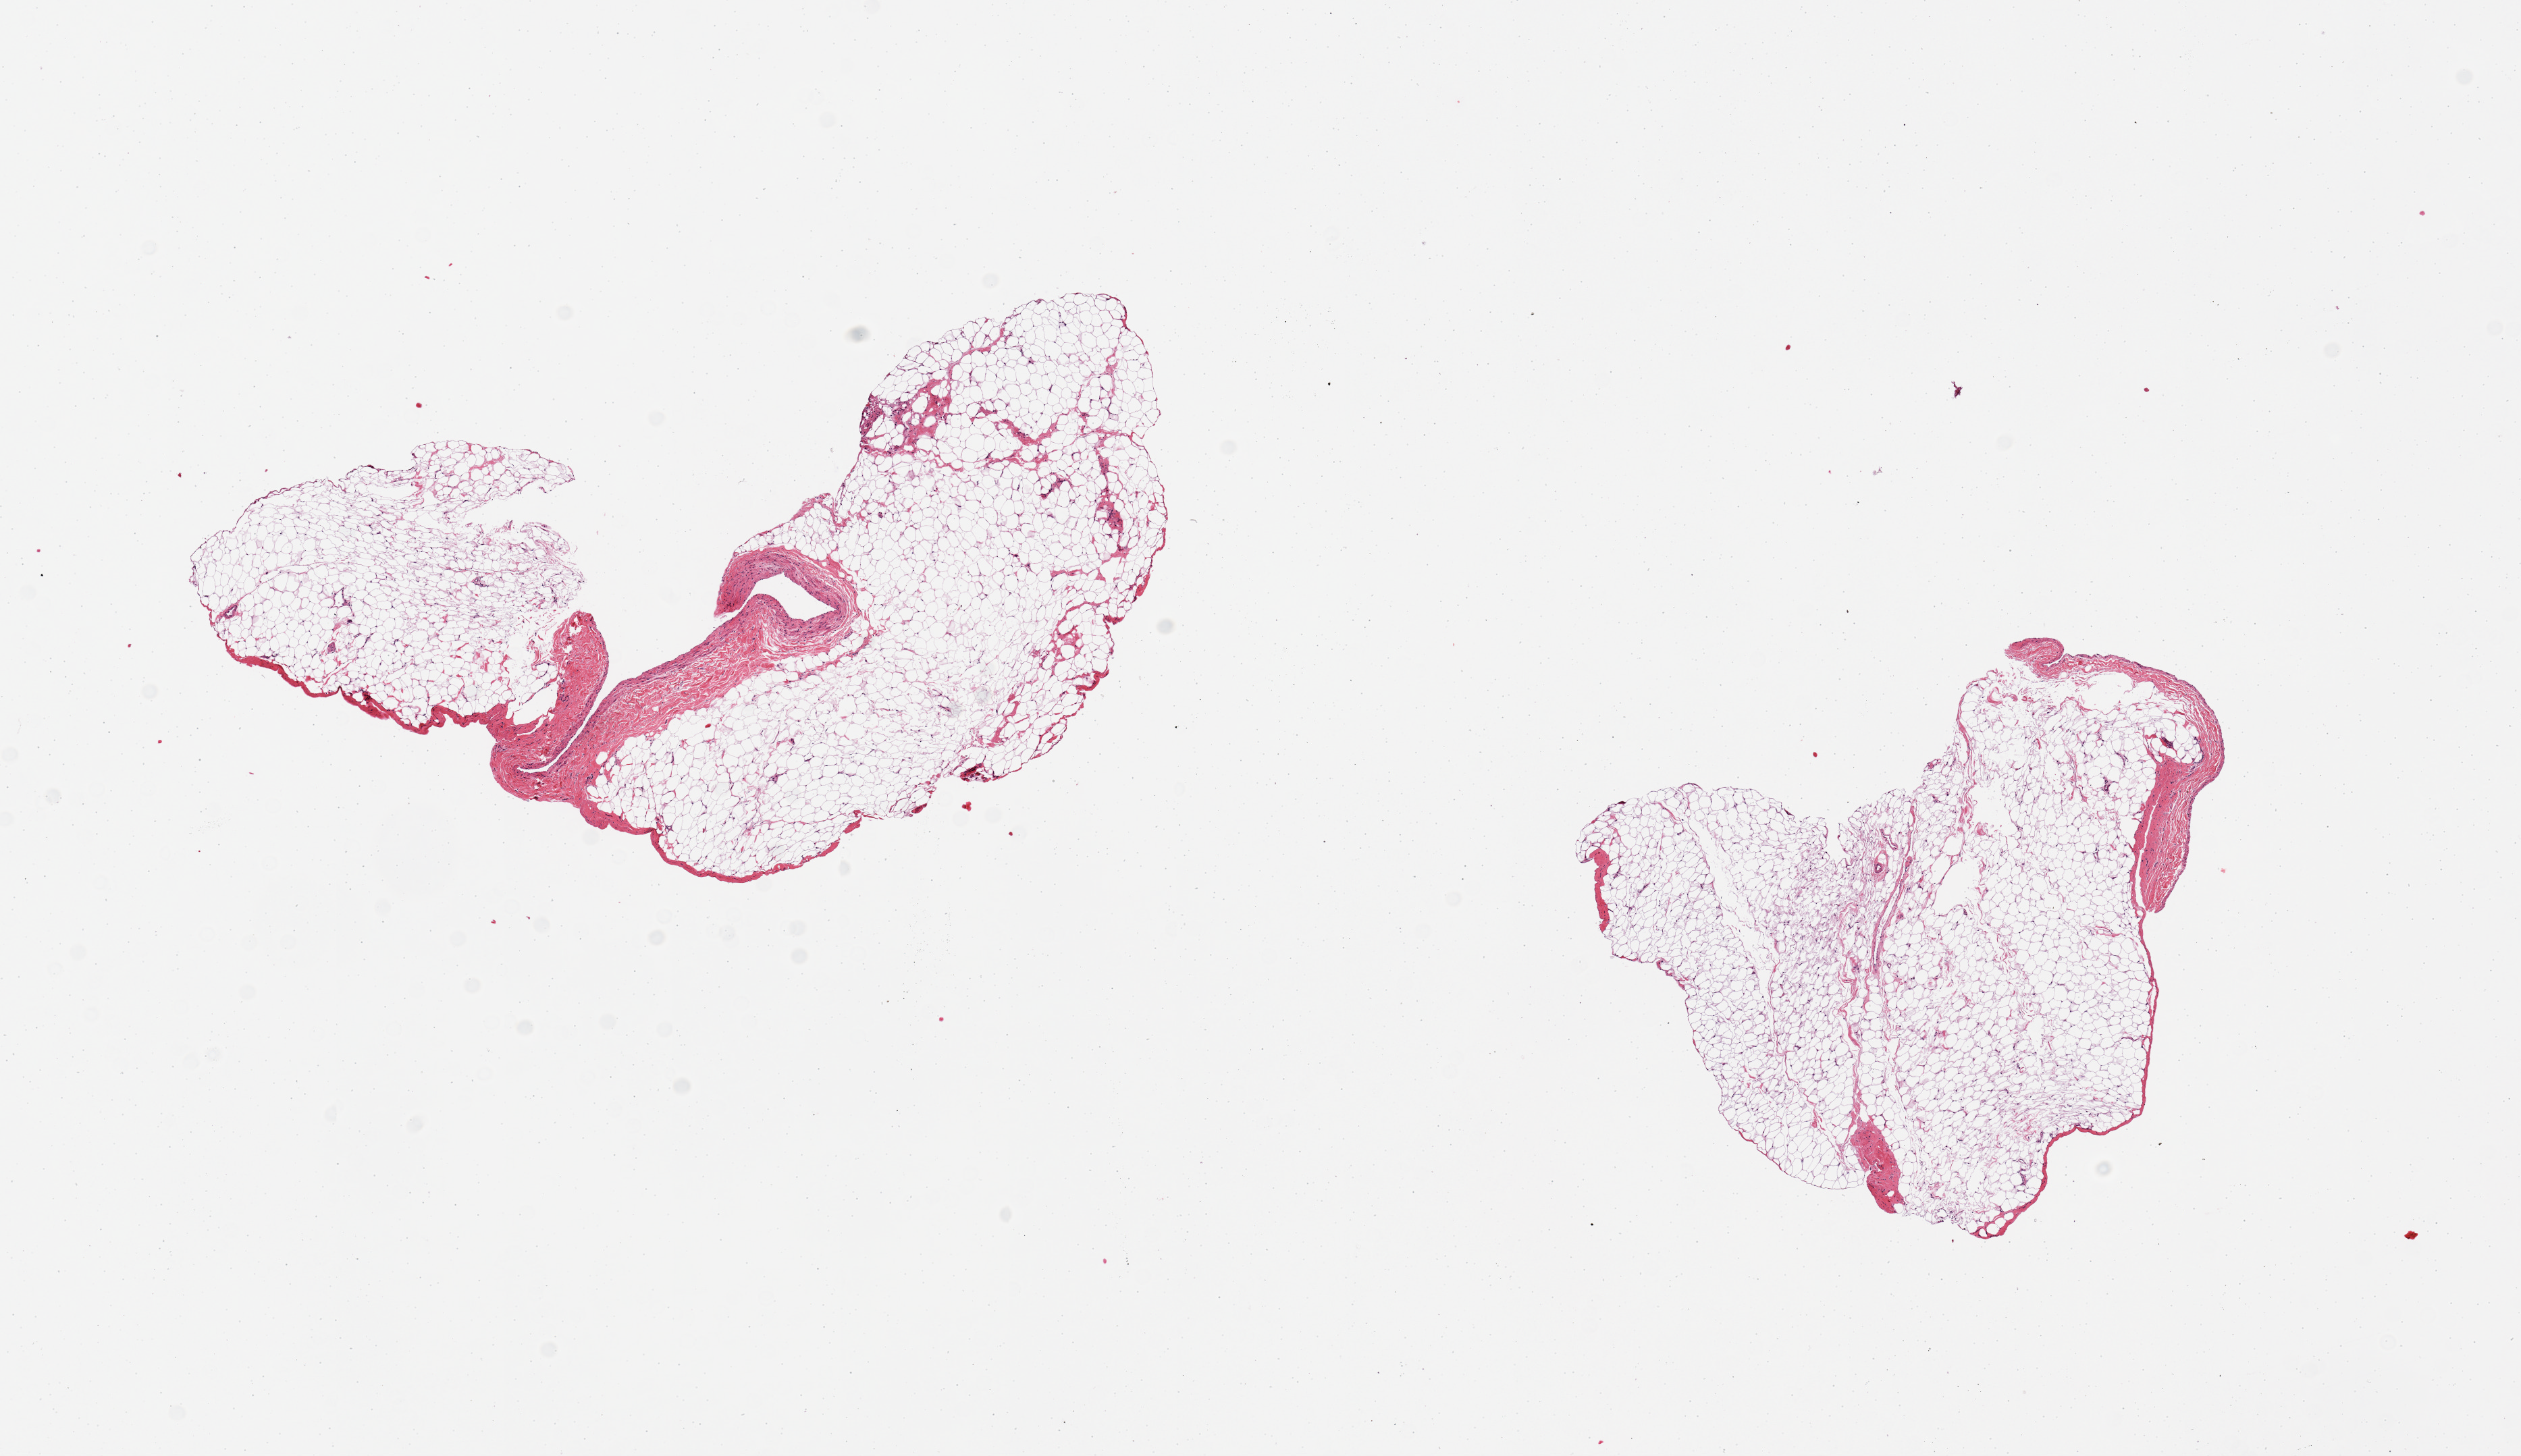
Whole-slide image, haematoxylin and eosin stain — low-resolution overview of the scanned area, about 14.8 x 8.5 mm, PAXgene-fixed paraffin-embedded (PFPE) section, section of coronary artery (target tissue), donor tissue sample. Female donor.
Pathologist's review note for this sample: 2 pieces, predominantly fat with portion of vein, not artery.